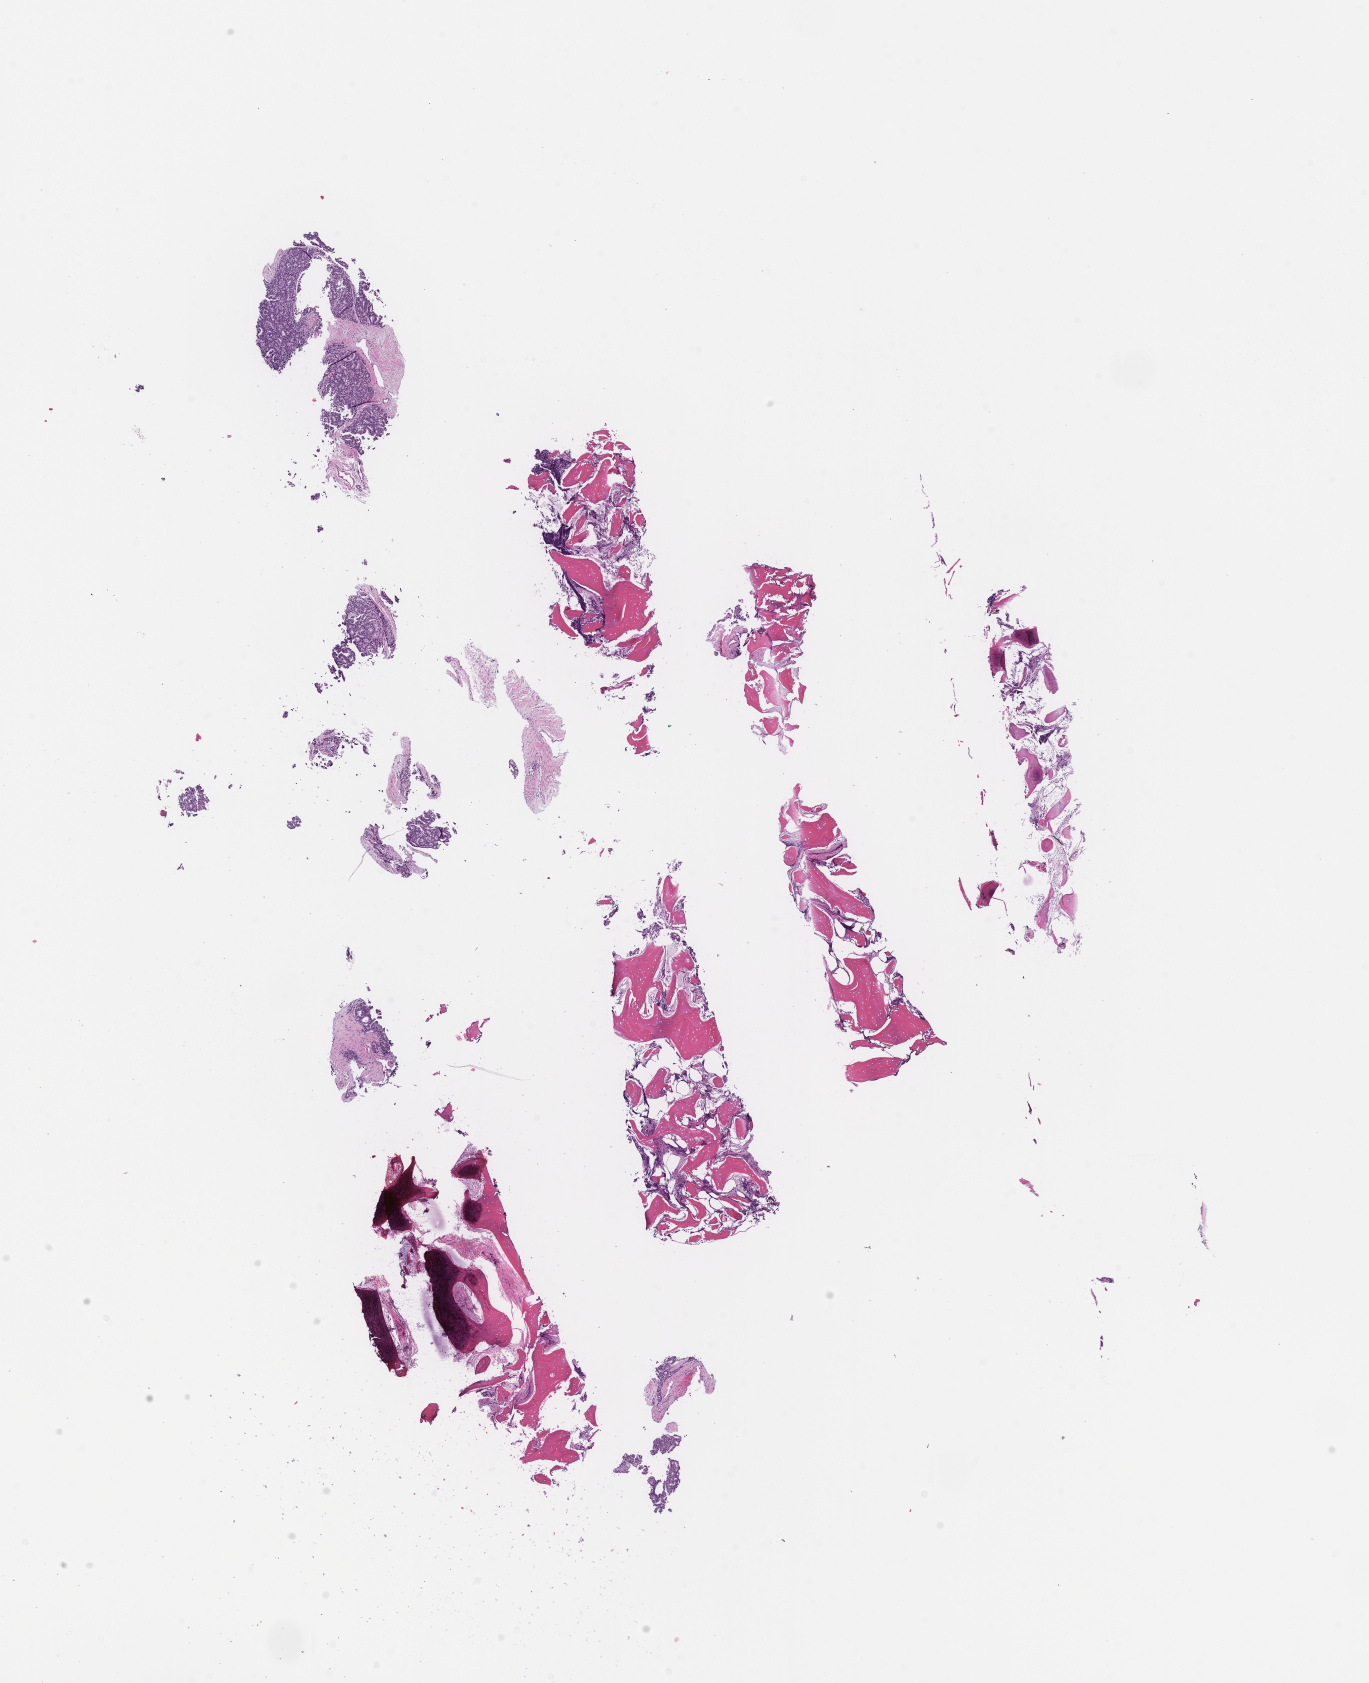
Whole-slide image, haematoxylin and eosin stain — low-resolution overview of the scanned area, about 11.1 x 13.6 mm. Formalin-fixed paraffin-embedded section. Tissue site: prostate. Archival tissue. Patient sex: male.
• this section: primary tumor
• diagnosis: Prostate Carcinoma